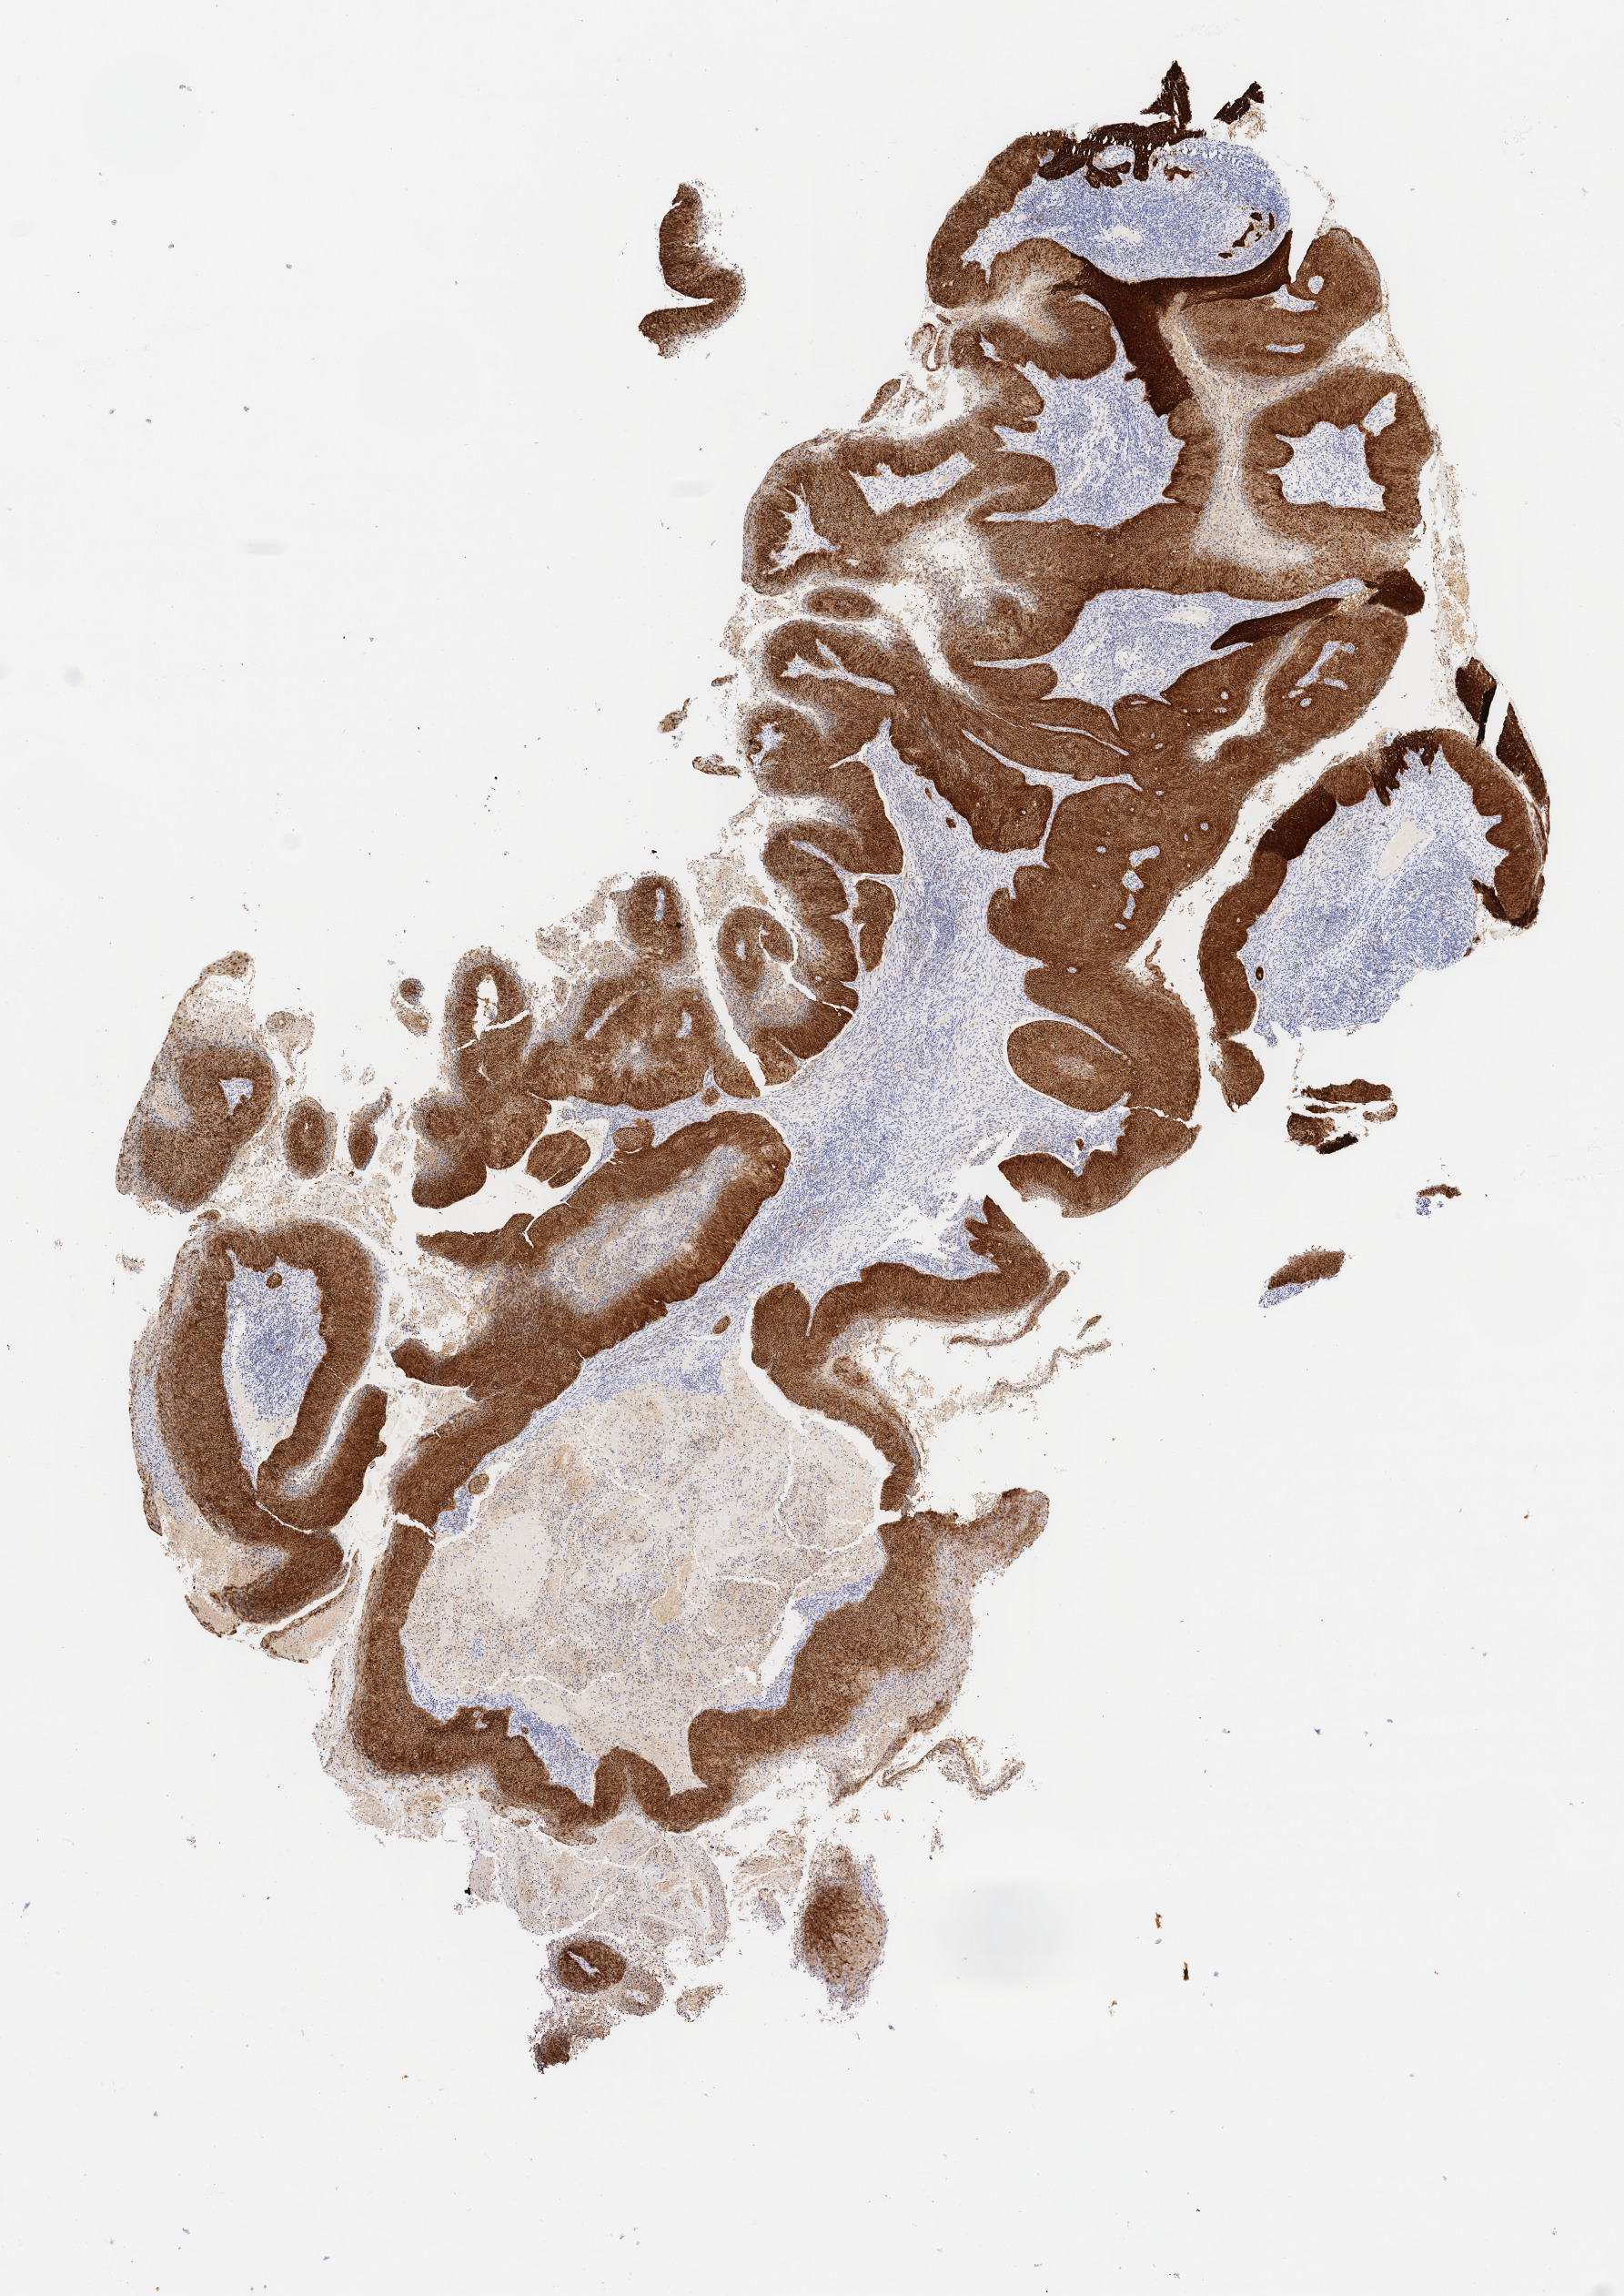
Immunohistochemistry (IHC) whole-slide image stained for p16 (p16INK4a) — shown as a low-resolution overview of the whole scanned area (about 7.1 x 10.0 mm), tumor tissue, anatomic site: cervix. Patient female; aged 49.
Histologic diagnosis: Squamous cell carcinoma, large cell, nonkeratinizing, NOS.